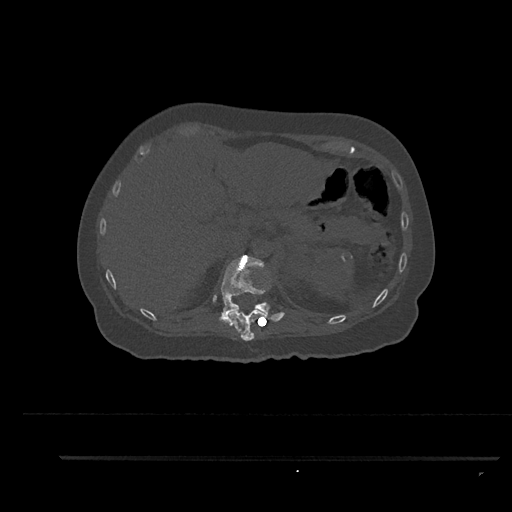
CT including the spine, one axial slice; position 287 of 797 along the scan axis; reconstruction kernel Br40s/3; 120 kVp; bone window (W 1800 / L 400 HU); 0.5 mm slice thickness; 512 × 512 image matrix. Female patient, age 44 years. From the clinical record (not read from this slice): primary cancer: renal; vertebrae with lytic lesions (as recorded): L1.
Annotated regions visible in this slice (semi-automatic segmentation, software-assisted and operator-edited):
- T11 vertebra: bounding box (x1, y1, x2, y2) in pixels: (230, 308, 265, 341)
- T12 vertebra: (219, 256, 284, 322)